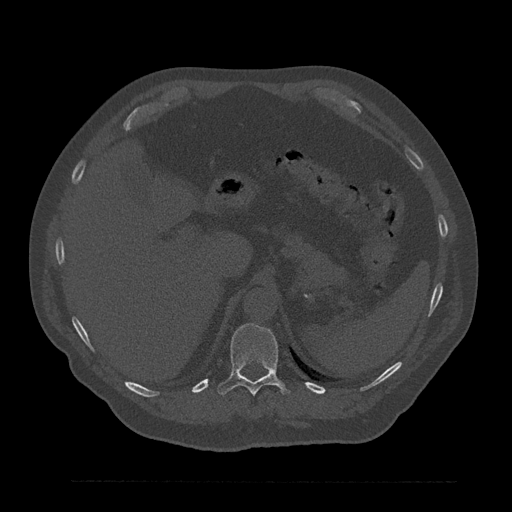
CT including the spine, one axial slice; reconstruction kernel Br40s/3; bone window (W 1800 / L 400 HU); 0.5 mm slice thickness; 512 × 512 image matrix. Patient: male, 61 years. Case-level facts recorded for this patient, not image findings: primary cancer: prostate.
Structures marked on this image (semi-automatic segmentation, software-assisted and operator-edited):
- T11 vertebra: bounding box [x1, y1, x2, y2] px = [217, 323, 289, 395]